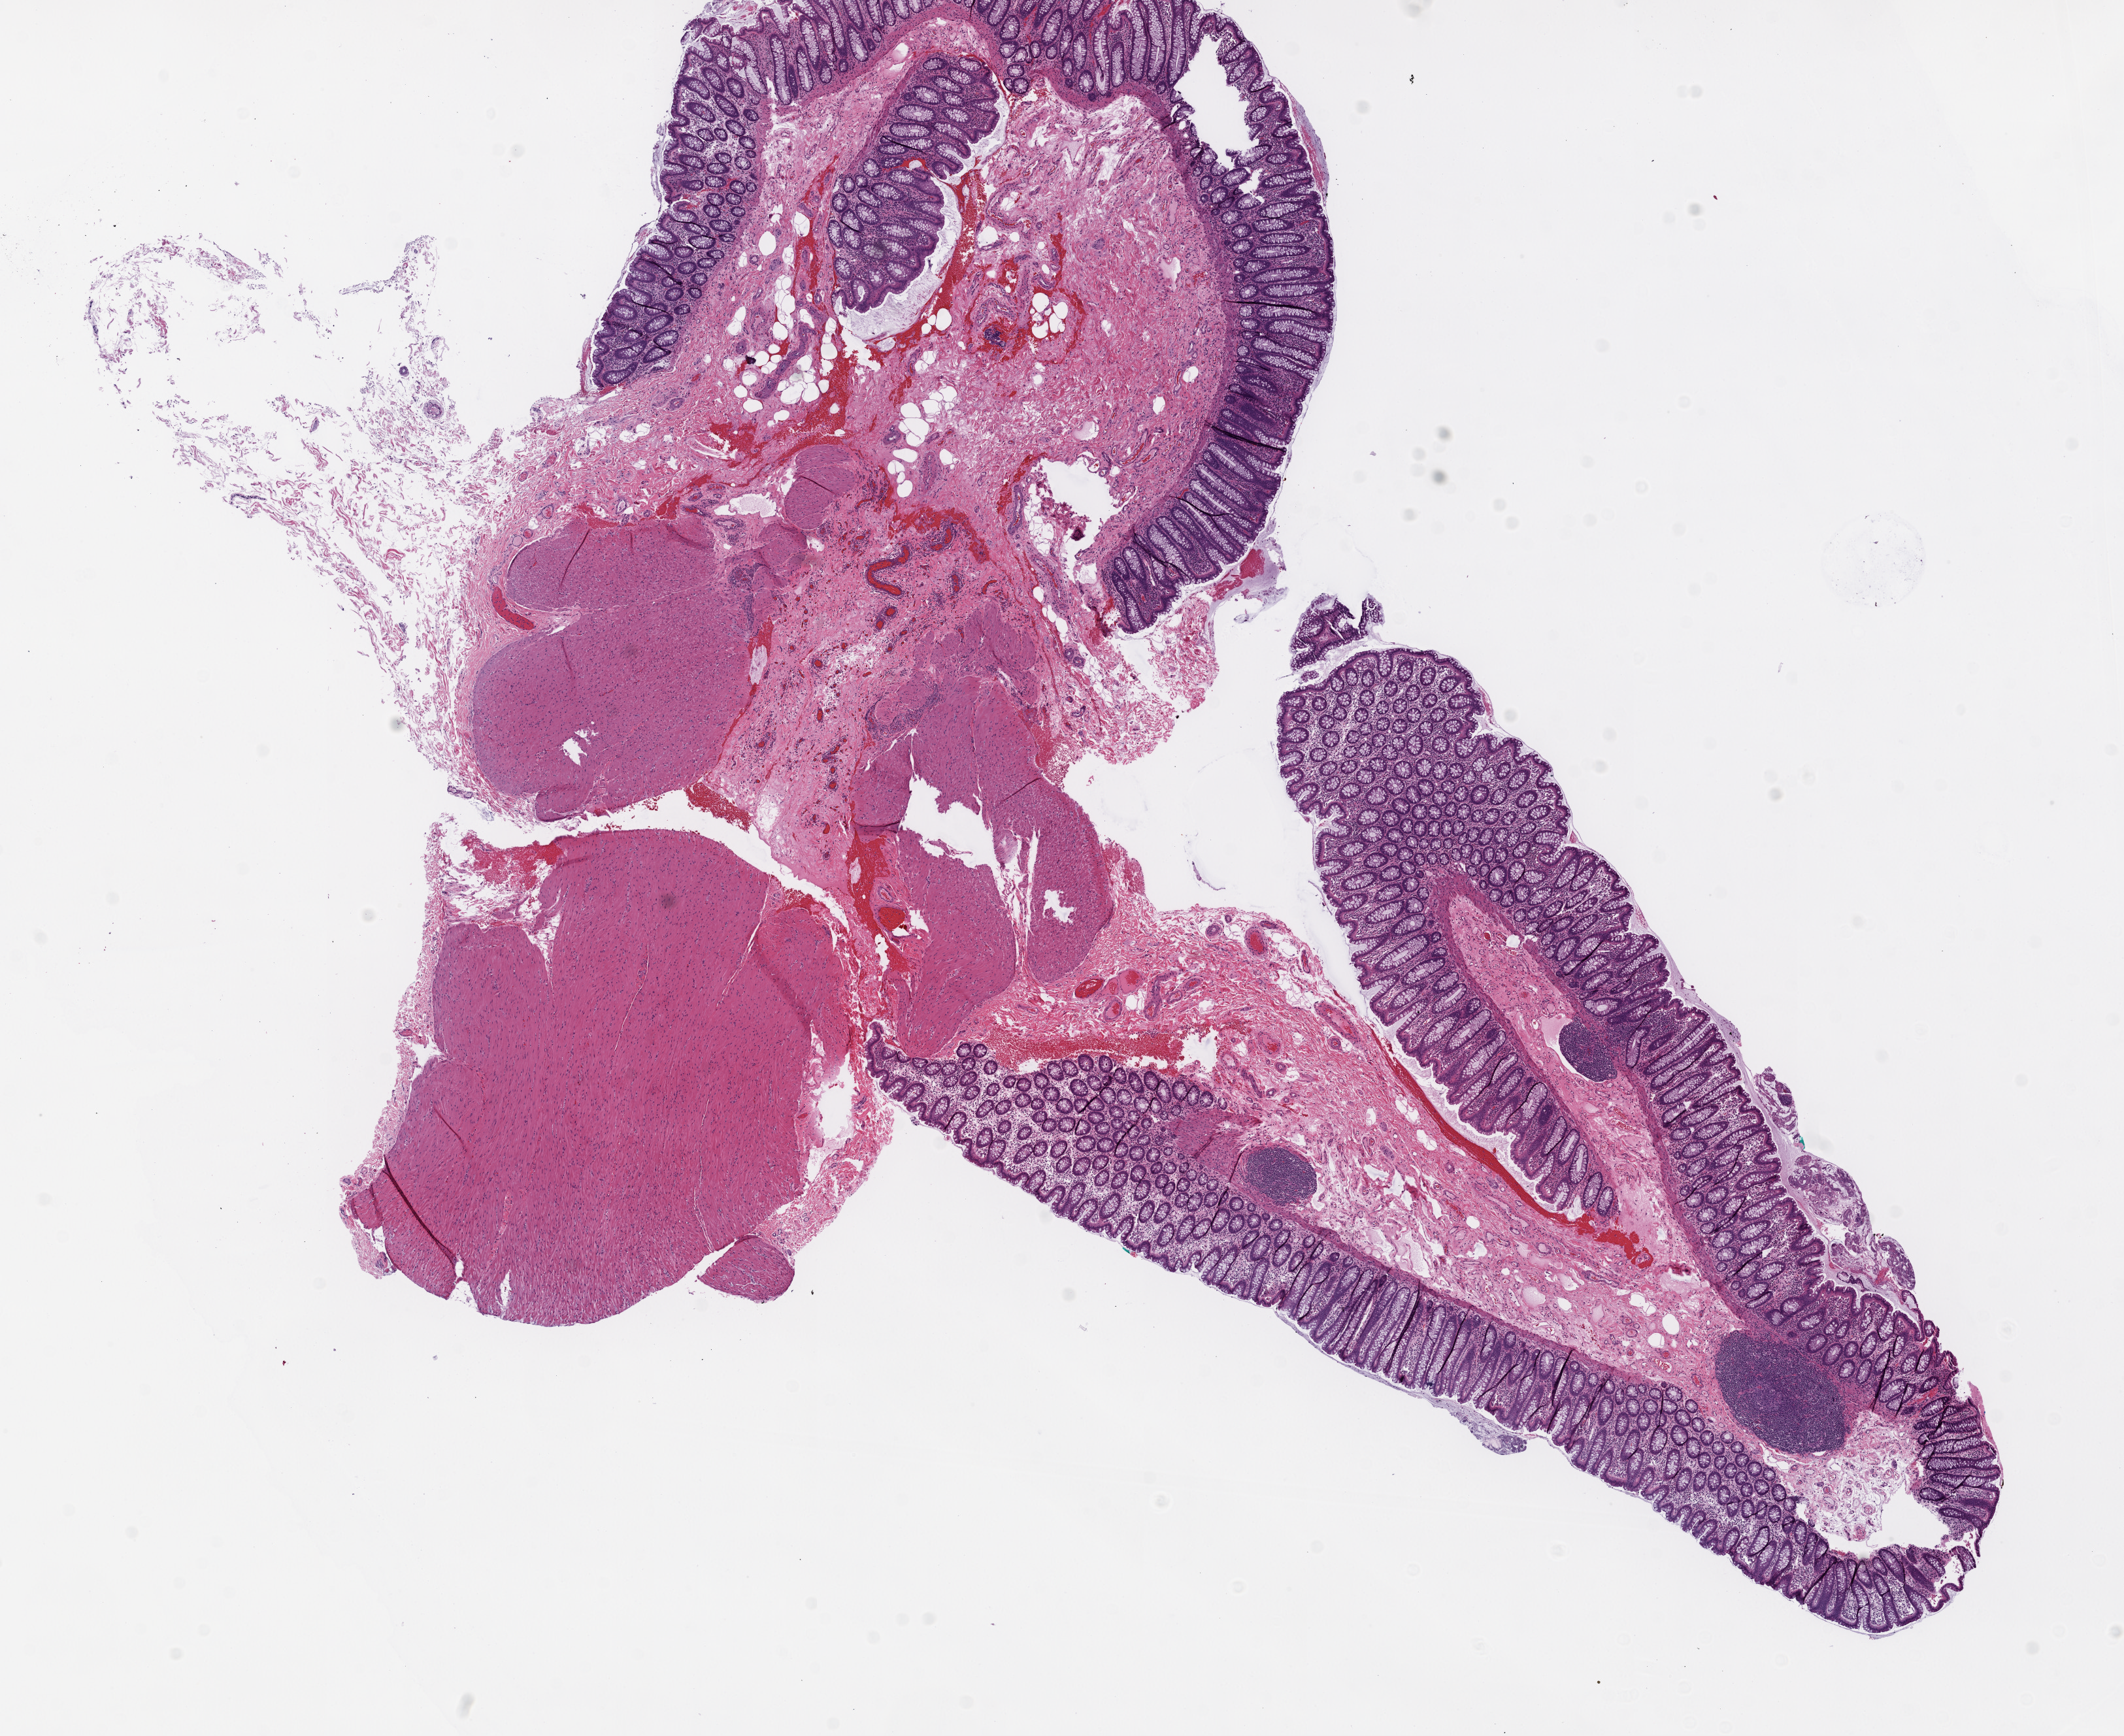
Digitized H&E-stained tissue section (whole slide) — low-resolution overview of the scanned area, about 13.0 x 10.7 mm (slide scanned at 20x); frozen section from the top of the tissue portion; sample: solid tissue normal (non-tumour tissue), colon. Patient: male, age at initial diagnosis 62 years.
- this section: solid tissue normal (non-tumour) sample from the same patient
- patient diagnosis: Adenocarcinoma, NOS